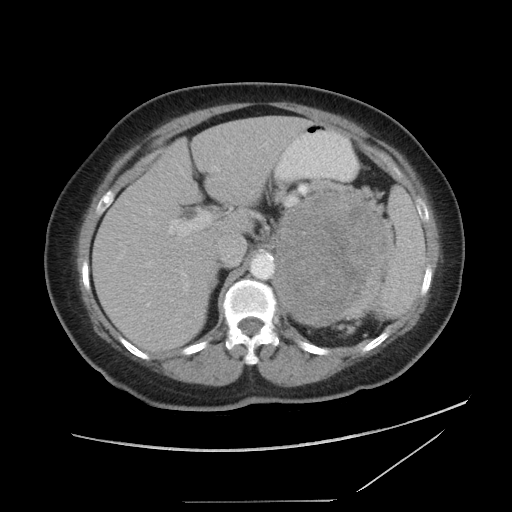
Contrast-enhanced abdominal CT, one axial slice; position 61 of 86 along the scan axis; reconstruction kernel STANDARD; intravenous contrast given; soft-tissue window (W 400 / L 40 HU); 5 mm slice thickness; 512 × 512 image matrix. Female patient, age 77 years. From the clinical record (not read from this slice): diagnosis: adrenocortical carcinoma; tumour side: left adrenal; tumour size at pathology: 13.1 cm; Ki-67 index: 10 %; stage (as recorded): 3.
Annotated regions visible in this slice (semi-automatically segmented with operator editing):
- mass: bounding box <275,193,389,324> (left, top, right, bottom; pixels)